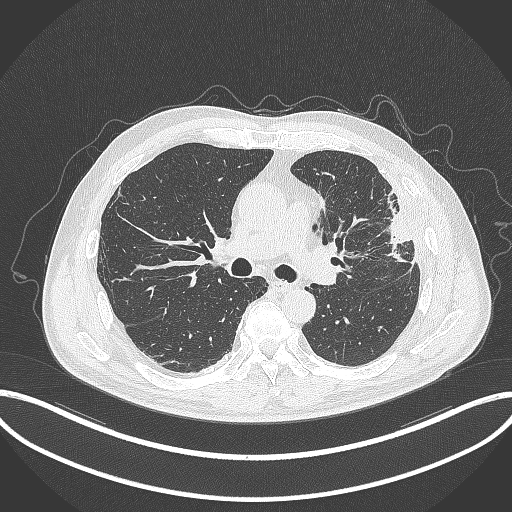
Chest CT, one axial slice. Slice 203 of 382 in the series (ordered by position). Lung window (W 1500 / L -600 HU). 1 mm slice thickness. 512 × 512 image matrix. Patient: male, 64 years. Case-level facts recorded for this patient, not image findings: clinical TNM (as recorded): T4 N1 M0; histopathological grade: G3.
Outlined on this slice (bounding box drawn by a radiologist):
- lung tumour (recorded histology: adenocarcinoma): bounding box (x1, y1, x2, y2) in pixels: (380, 193, 417, 268)